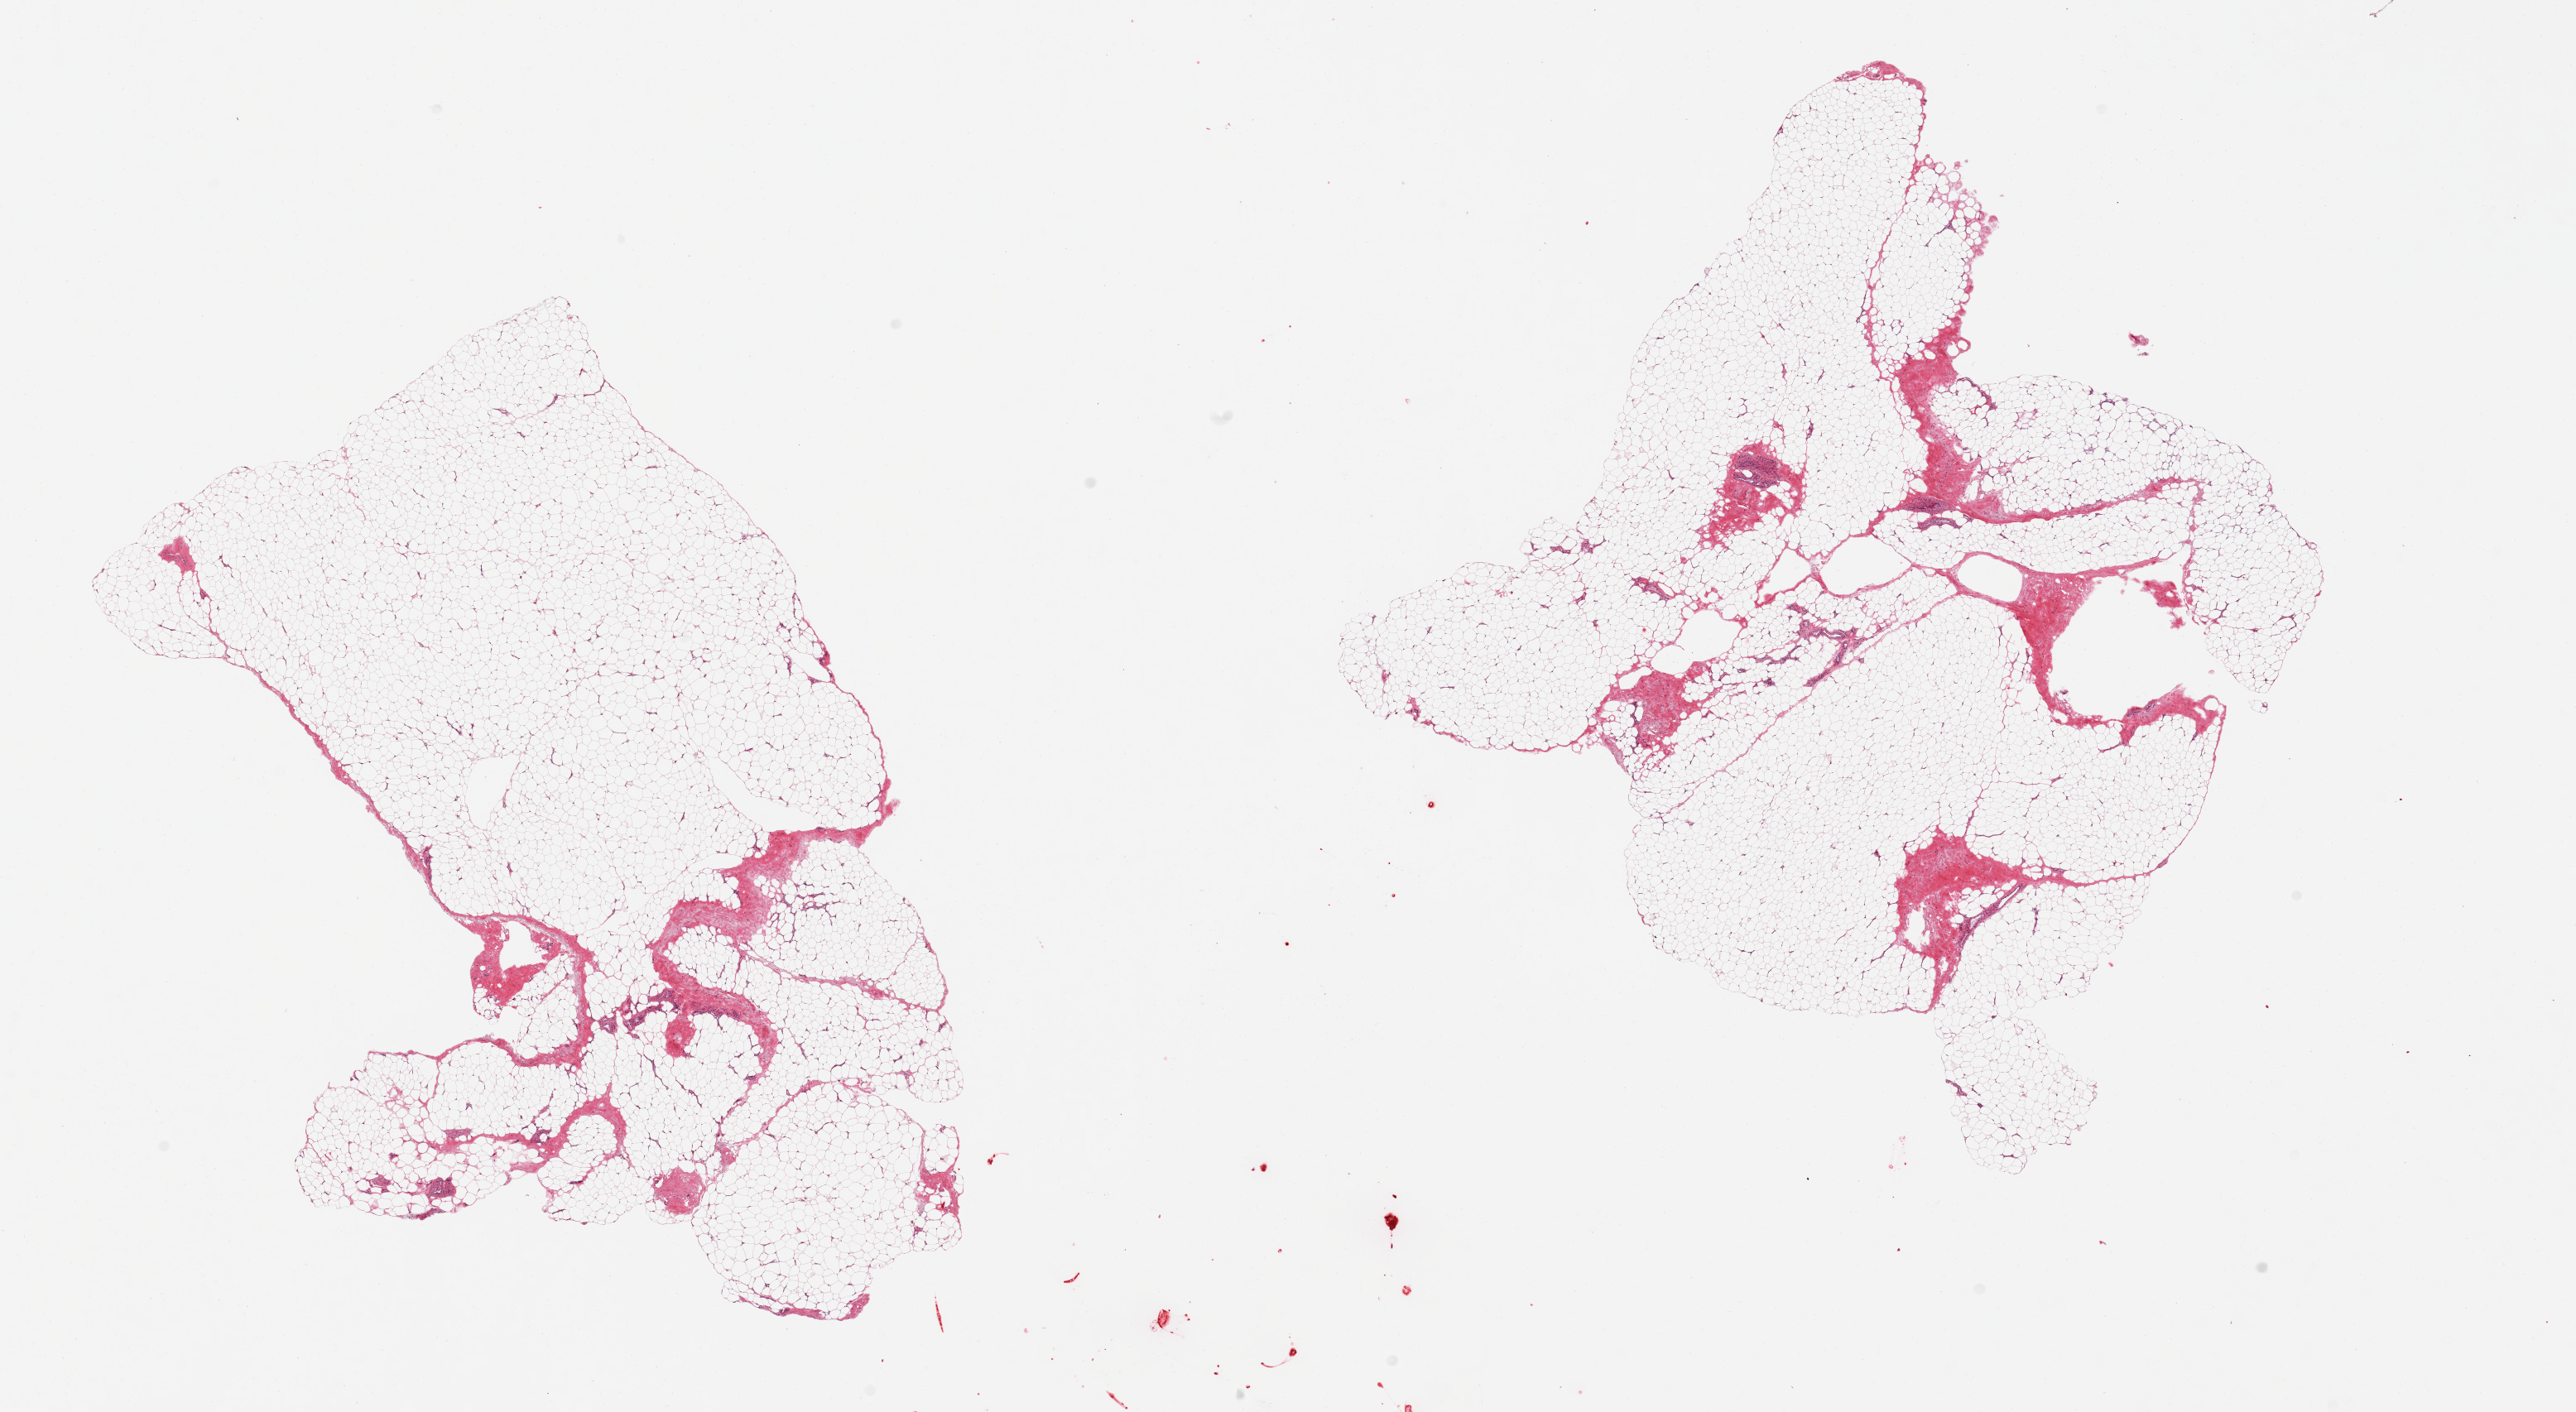
Digitized hematoxylin and eosin (H&E)-stained section, low-resolution overview of the scanned area, about 24.6 x 13.5 mm, PAXgene-fixed paraffin-embedded (PFPE) section, sampled site (target tissue): adipose tissue, donor tissue sample. Donor sex: male.
Pathologist's review note for this sample: 2 pieces; fat with 10% to 20% of fibrovascular tissue.